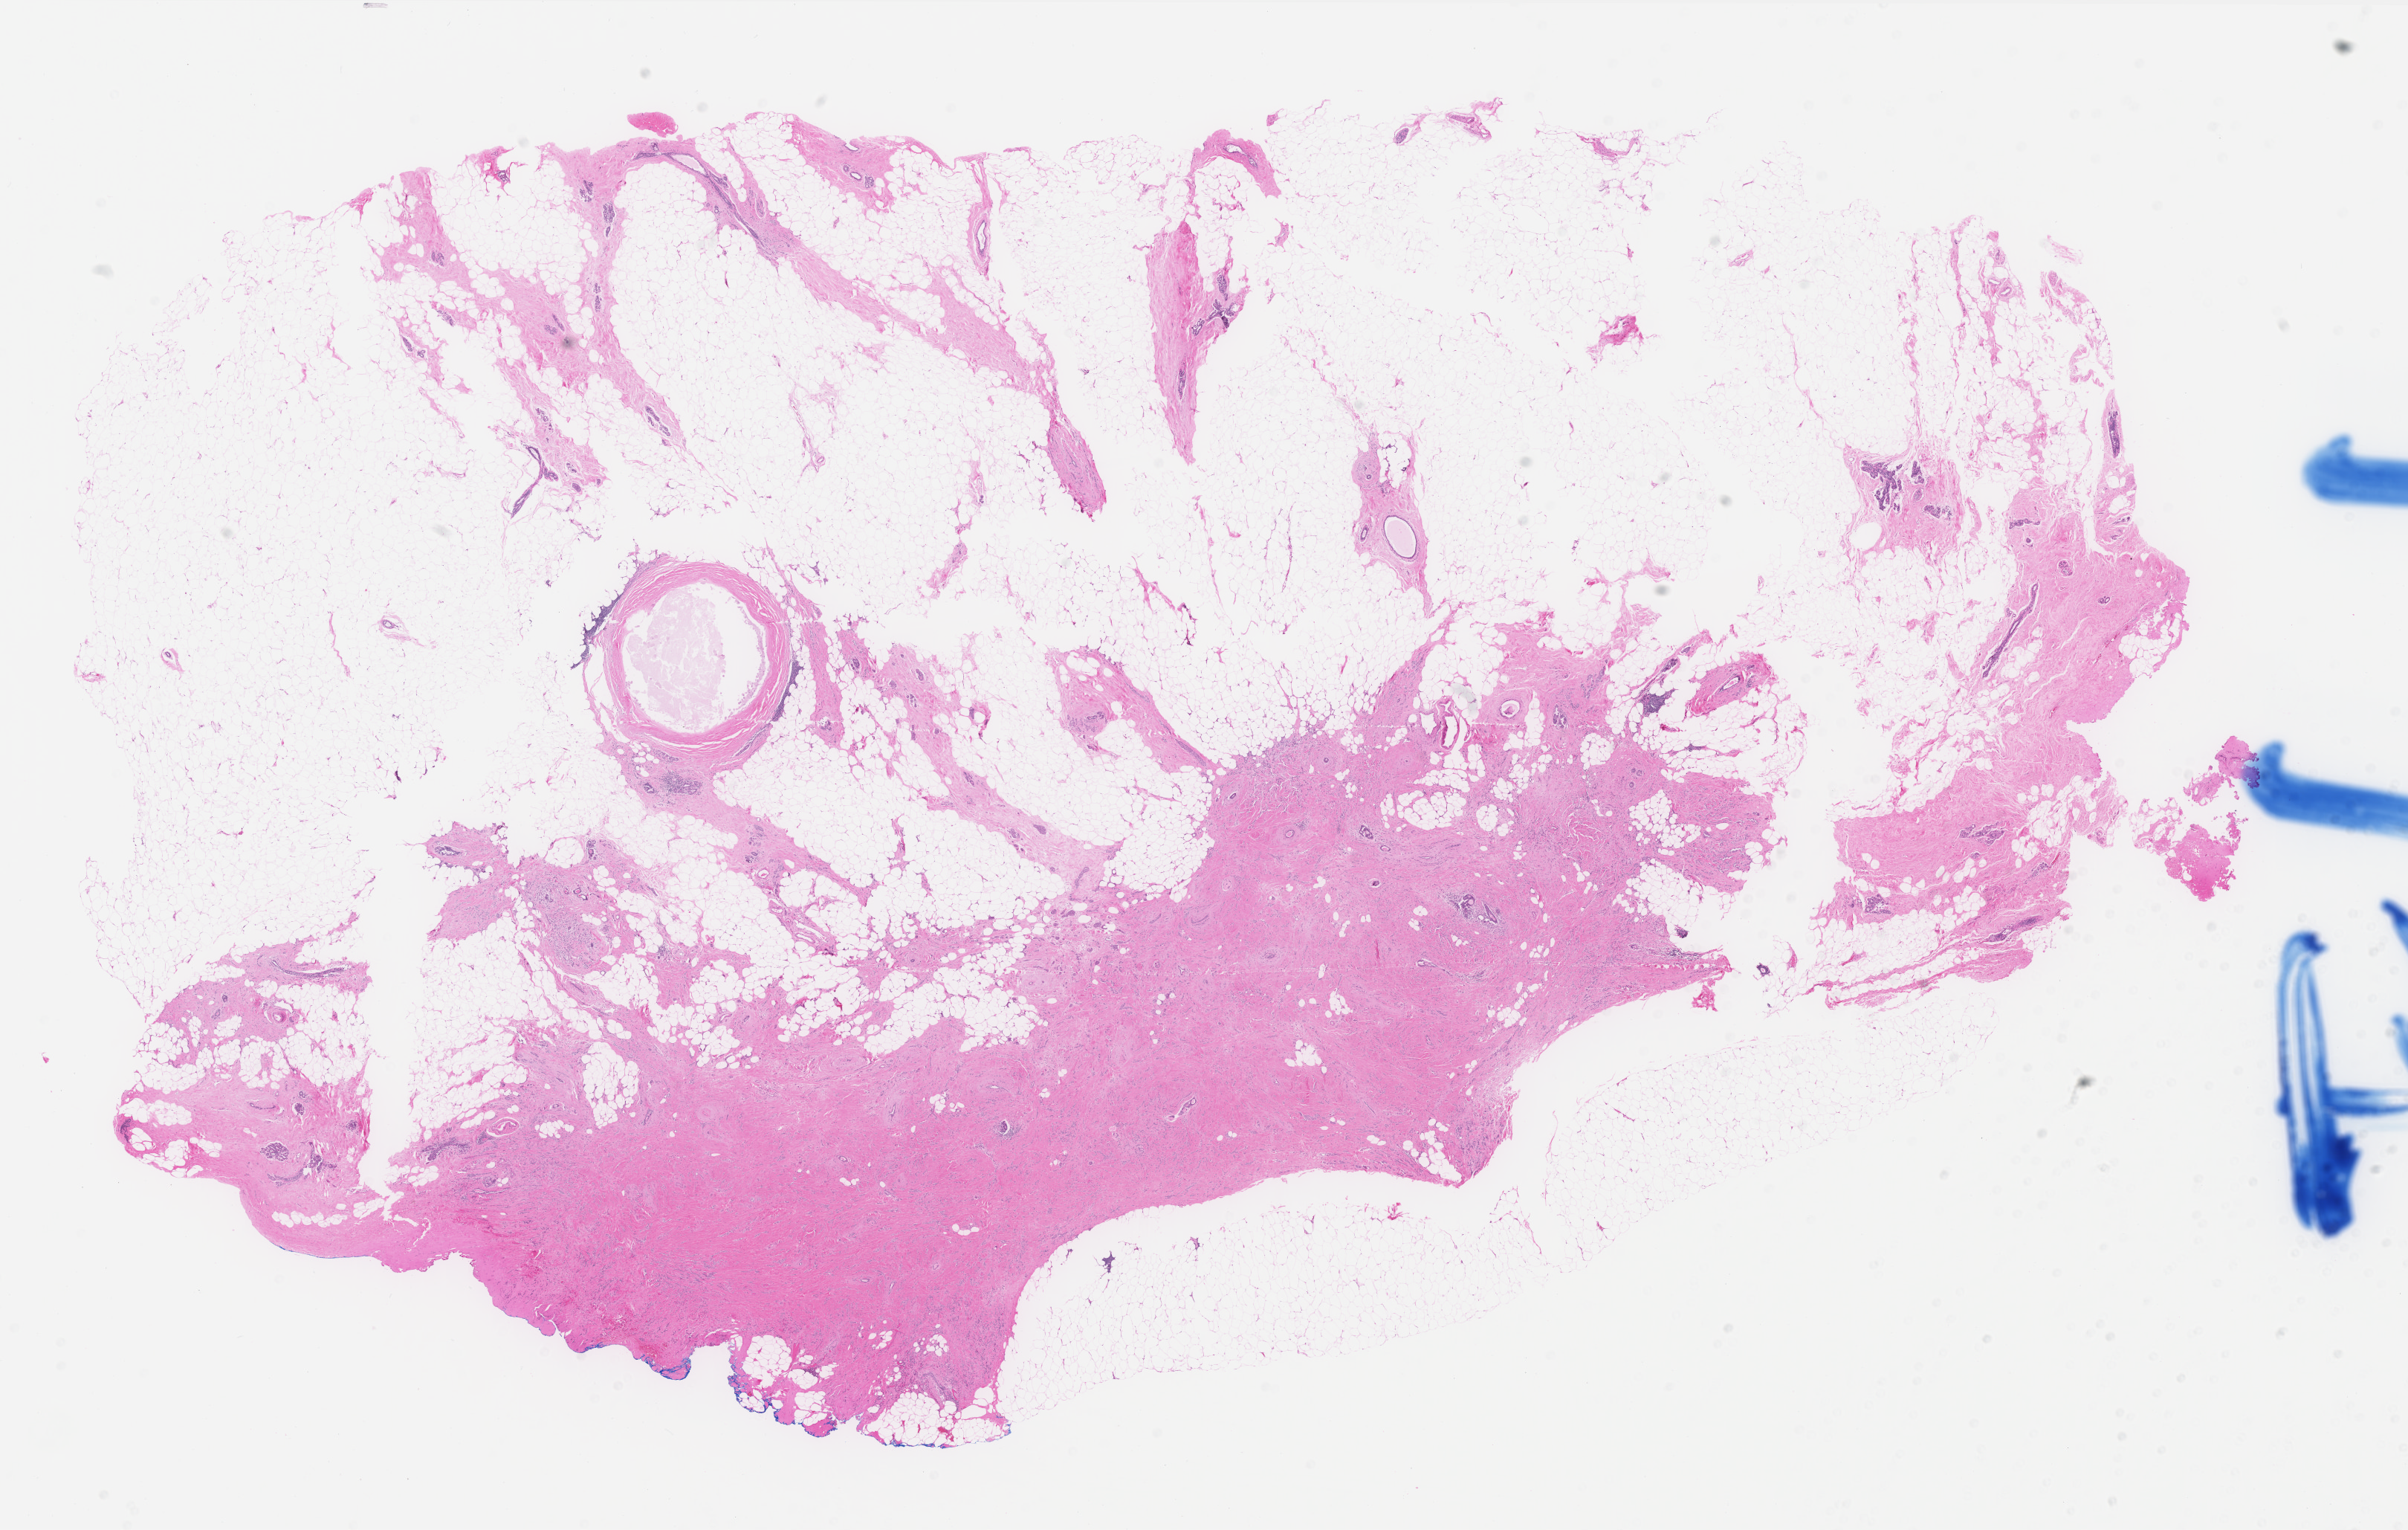
H&E whole-slide image — low-resolution overview of the scanned area, about 26.0 x 16.5 mm; FFPE section; breast, primary tumour sample. Patient: female, age at initial diagnosis 42 years.
Diagnosis: Infiltrating duct carcinoma, NOS.